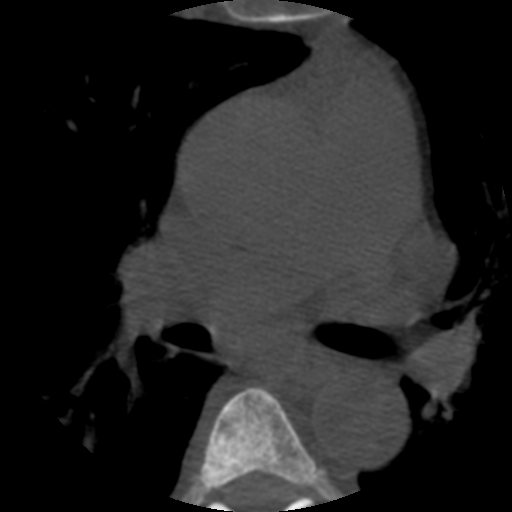
CT including the spine, one axial slice; slice 369 of 508 in the series (ordered by position); 120 kVp; bone window (W 1800 / L 400 HU); 1.25 mm slice thickness; 512 × 512 image matrix, field of view 160 × 160 mm. Patient age 57 years. From the clinical record (not read from this slice): primary cancer: prostate.
Annotated regions visible in this slice (semi-automatically segmented with operator editing):
- T5 vertebra: box from (x=195, y=387) to (x=321, y=490) px
- T6 vertebra: (x=209, y=492)–(x=314, y=512)